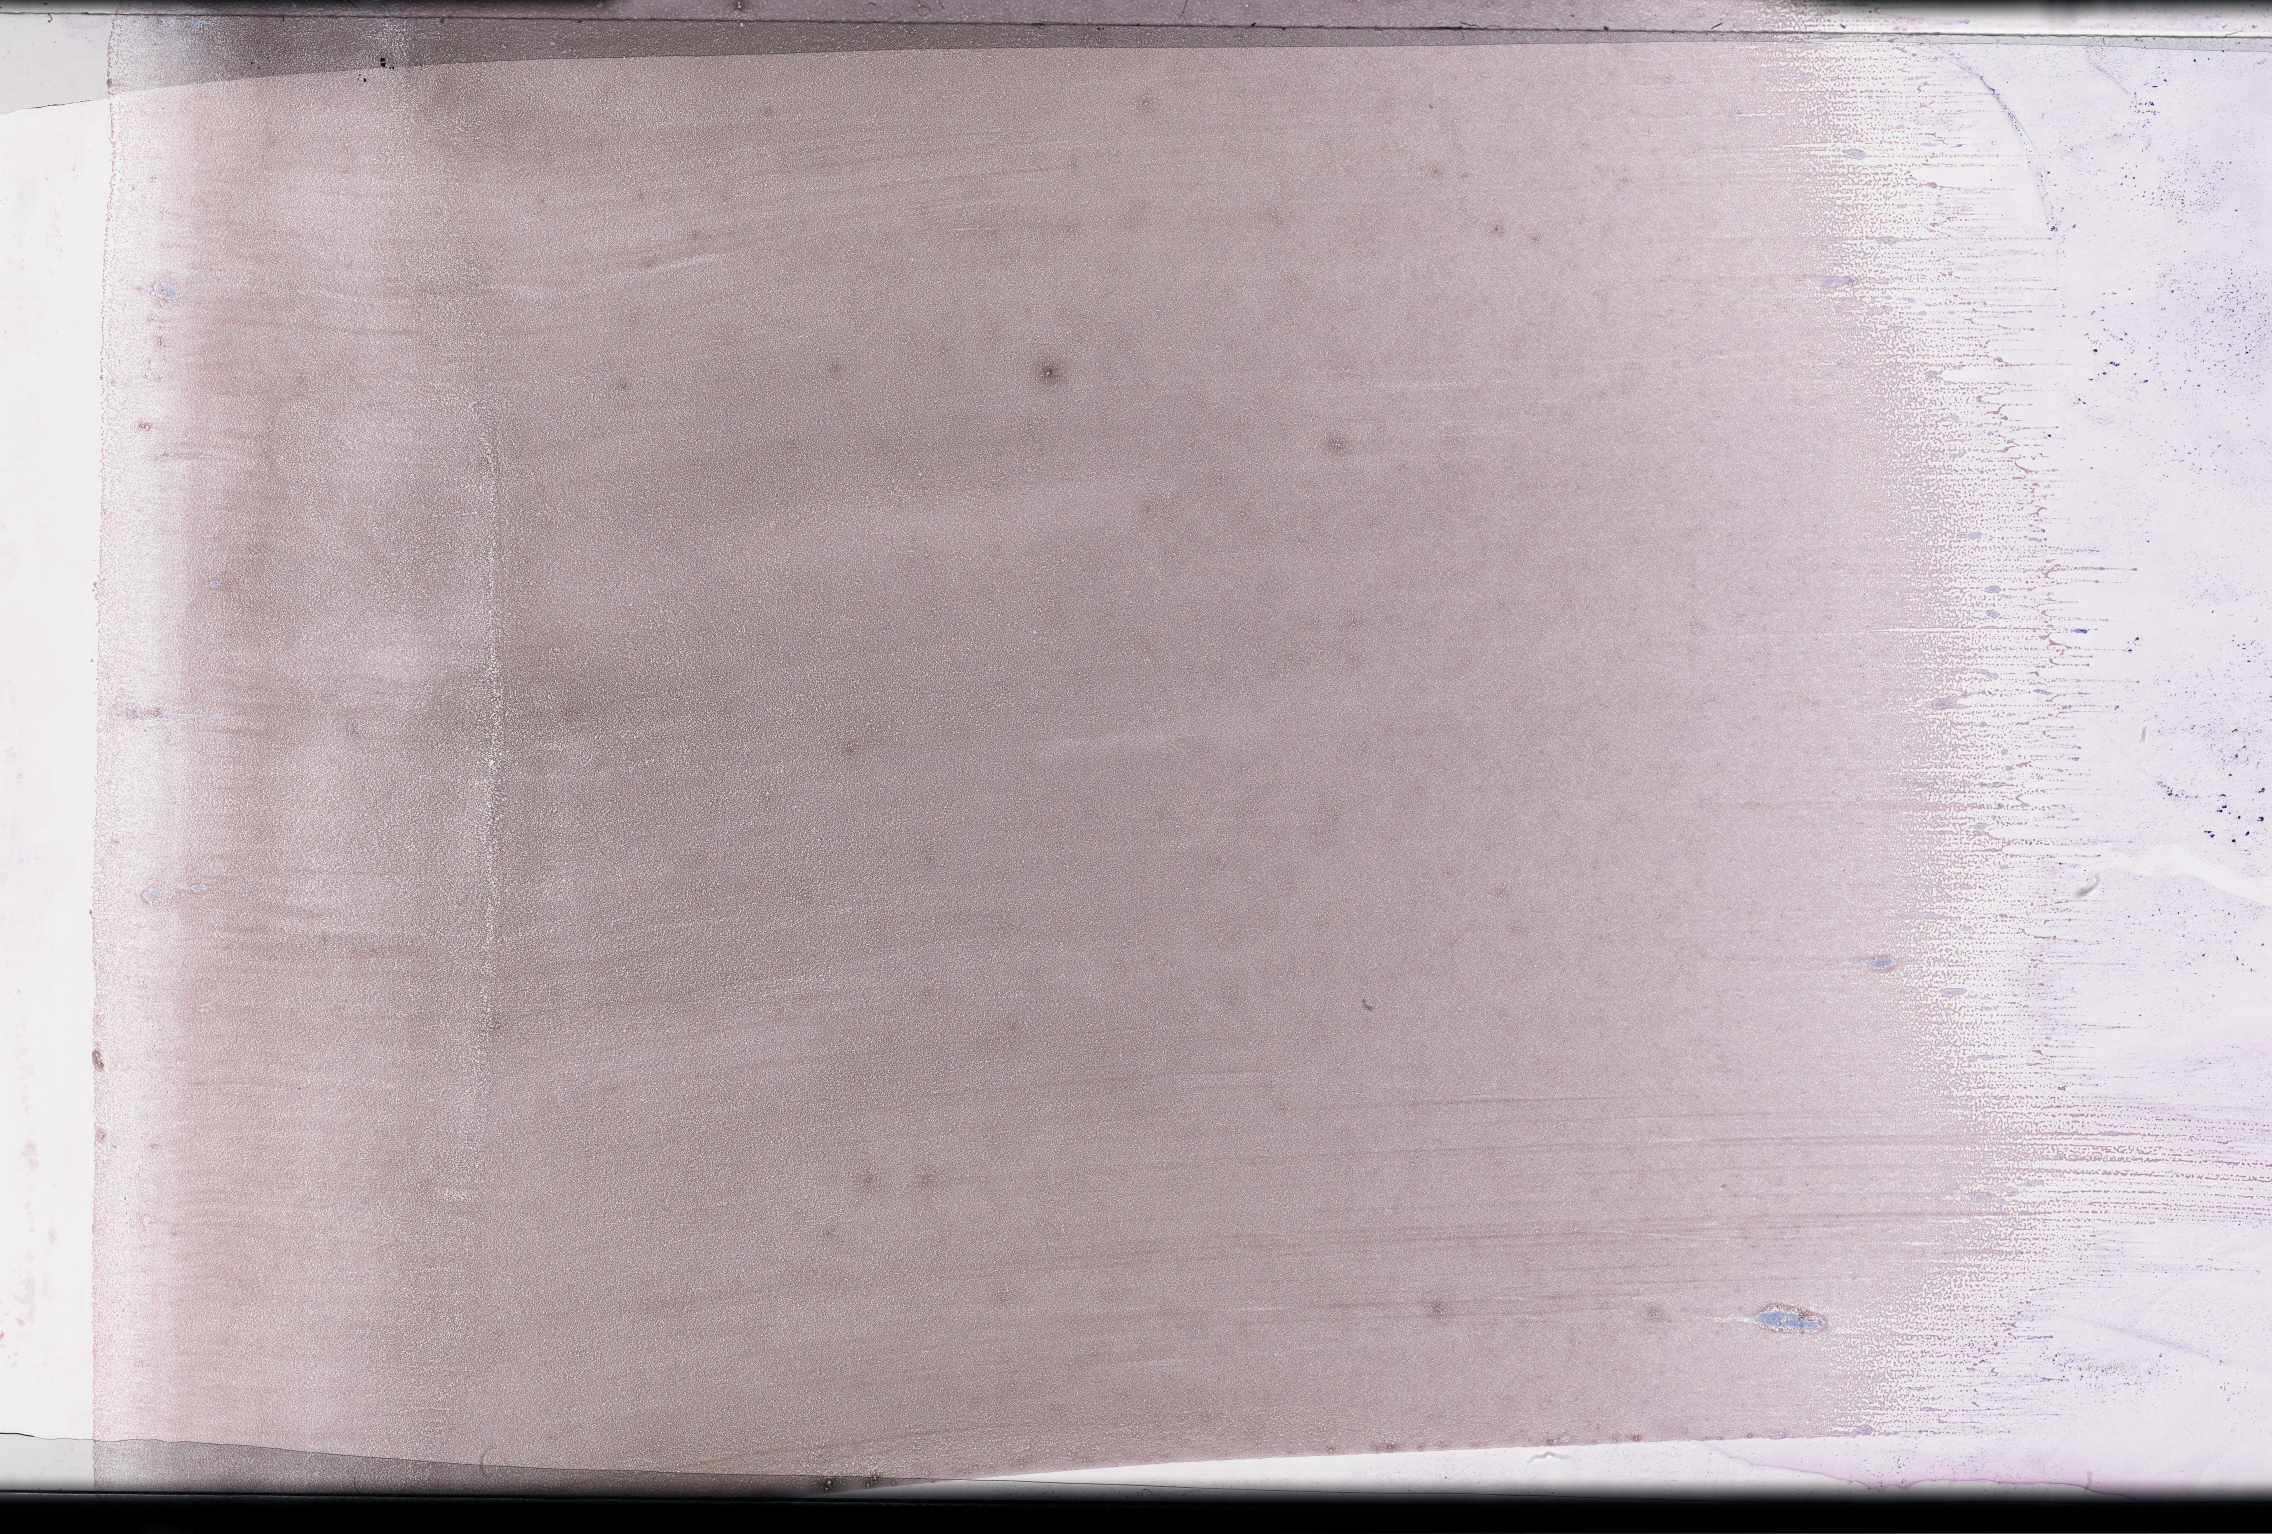
Whole-slide image of a whole blood smear, Wright–Giemsa stain — whole scanned area (about 36.7 x 24.8 mm) shown as a low-resolution overview. Smear from an EDTA sample. Specimen time point: collected on treatment. Patient: male.
From a patient with: Plasma Cell Myeloma.